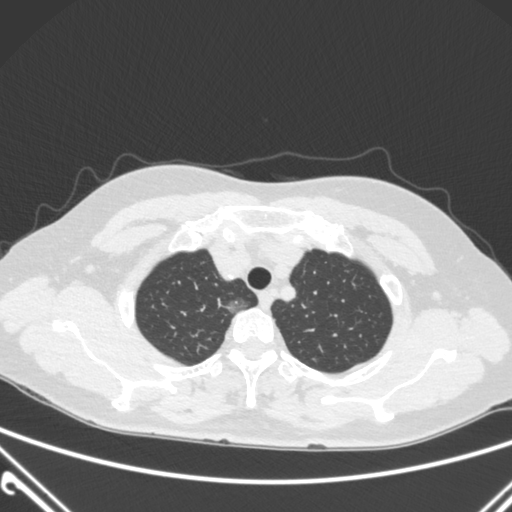
Chest CT, one axial slice; slice 241 of 300 in the series (ordered by position); lung window (W 1500 / L -600 HU); 1 mm slice thickness; 512 × 512 image matrix. Patient: female, 54 years. Case-level facts recorded for this patient, not image findings: clinical TNM (as recorded): T1a N0 M0.
Annotated regions visible in this slice (bounding box drawn by a radiologist):
- lung tumour (recorded histology: adenocarcinoma): box from (x=219, y=294) to (x=253, y=325) px